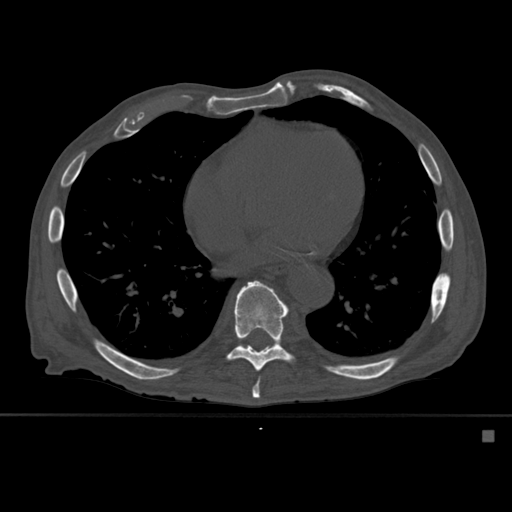
CT including the spine, one axial slice; position 334 of 527 along the scan axis; bone window (W 1800 / L 400 HU); 512 × 512 image matrix. Patient: male, 78 years. Case-level facts recorded for this patient, not image findings: primary cancer: prostate.
Annotated regions visible in this slice (semi-automatically segmented with operator editing):
- T8 vertebra: bounding box <252,380,260,399> (left, top, right, bottom; pixels)
- T9 vertebra: <226,280,294,387>